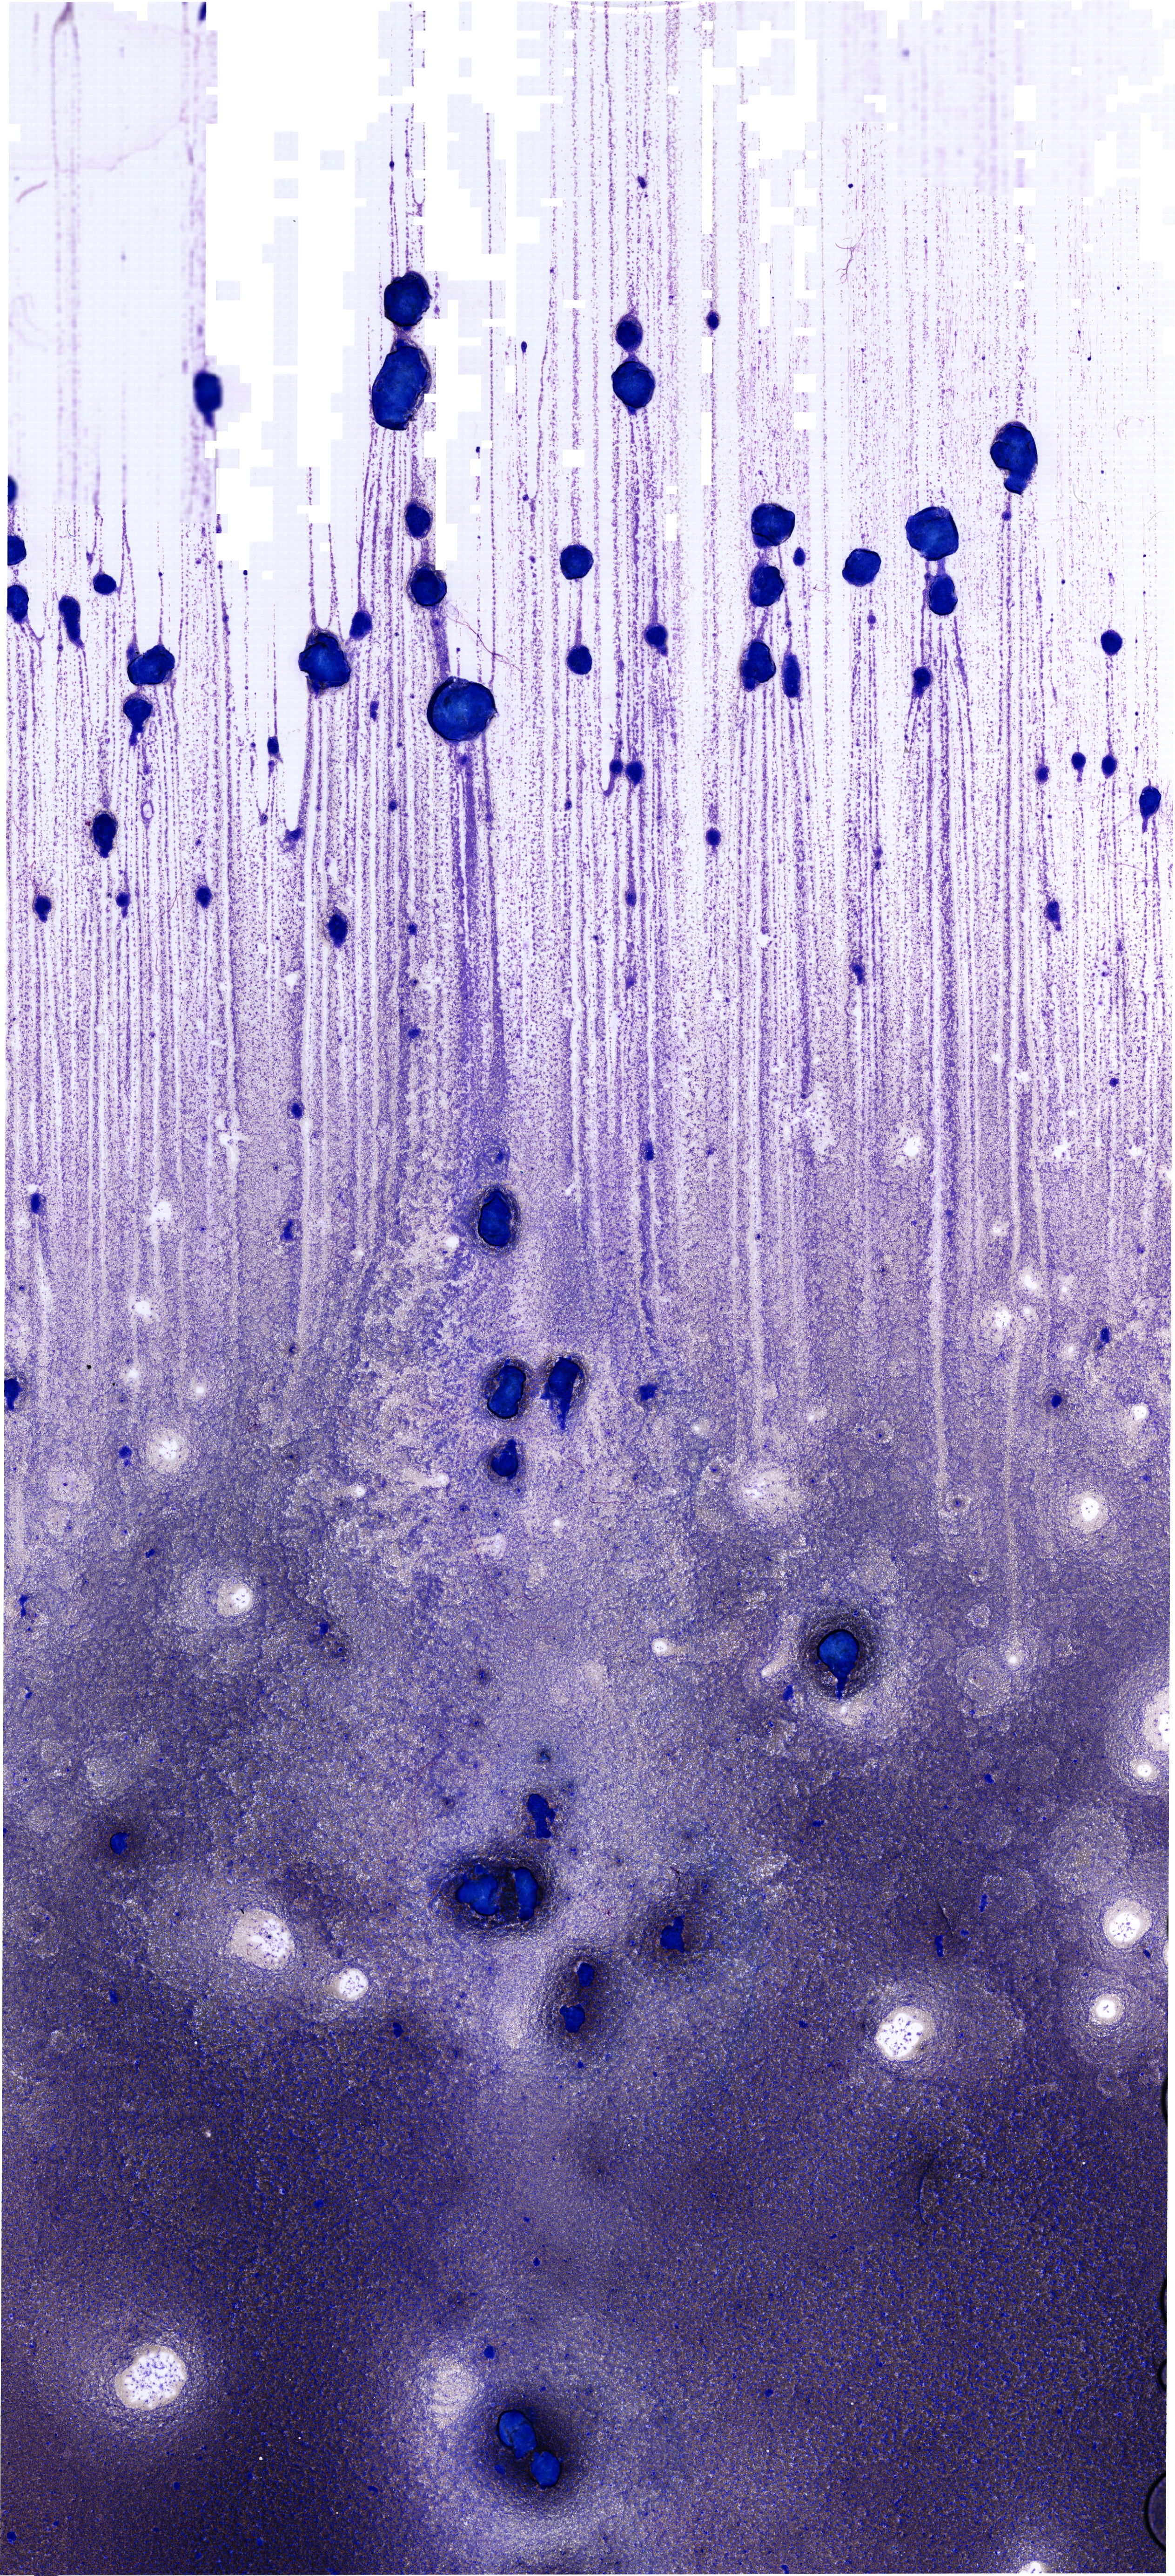
Whole-slide image of a May-Grünwald–Giemsa-stained bone marrow aspirate smear — a low-resolution overview of the entire scanned area, about 19.7 x 43.2 mm. Patient sex: male.
* diagnosis: Mixed Phenotype Acute Leukemia, B/Myeloid